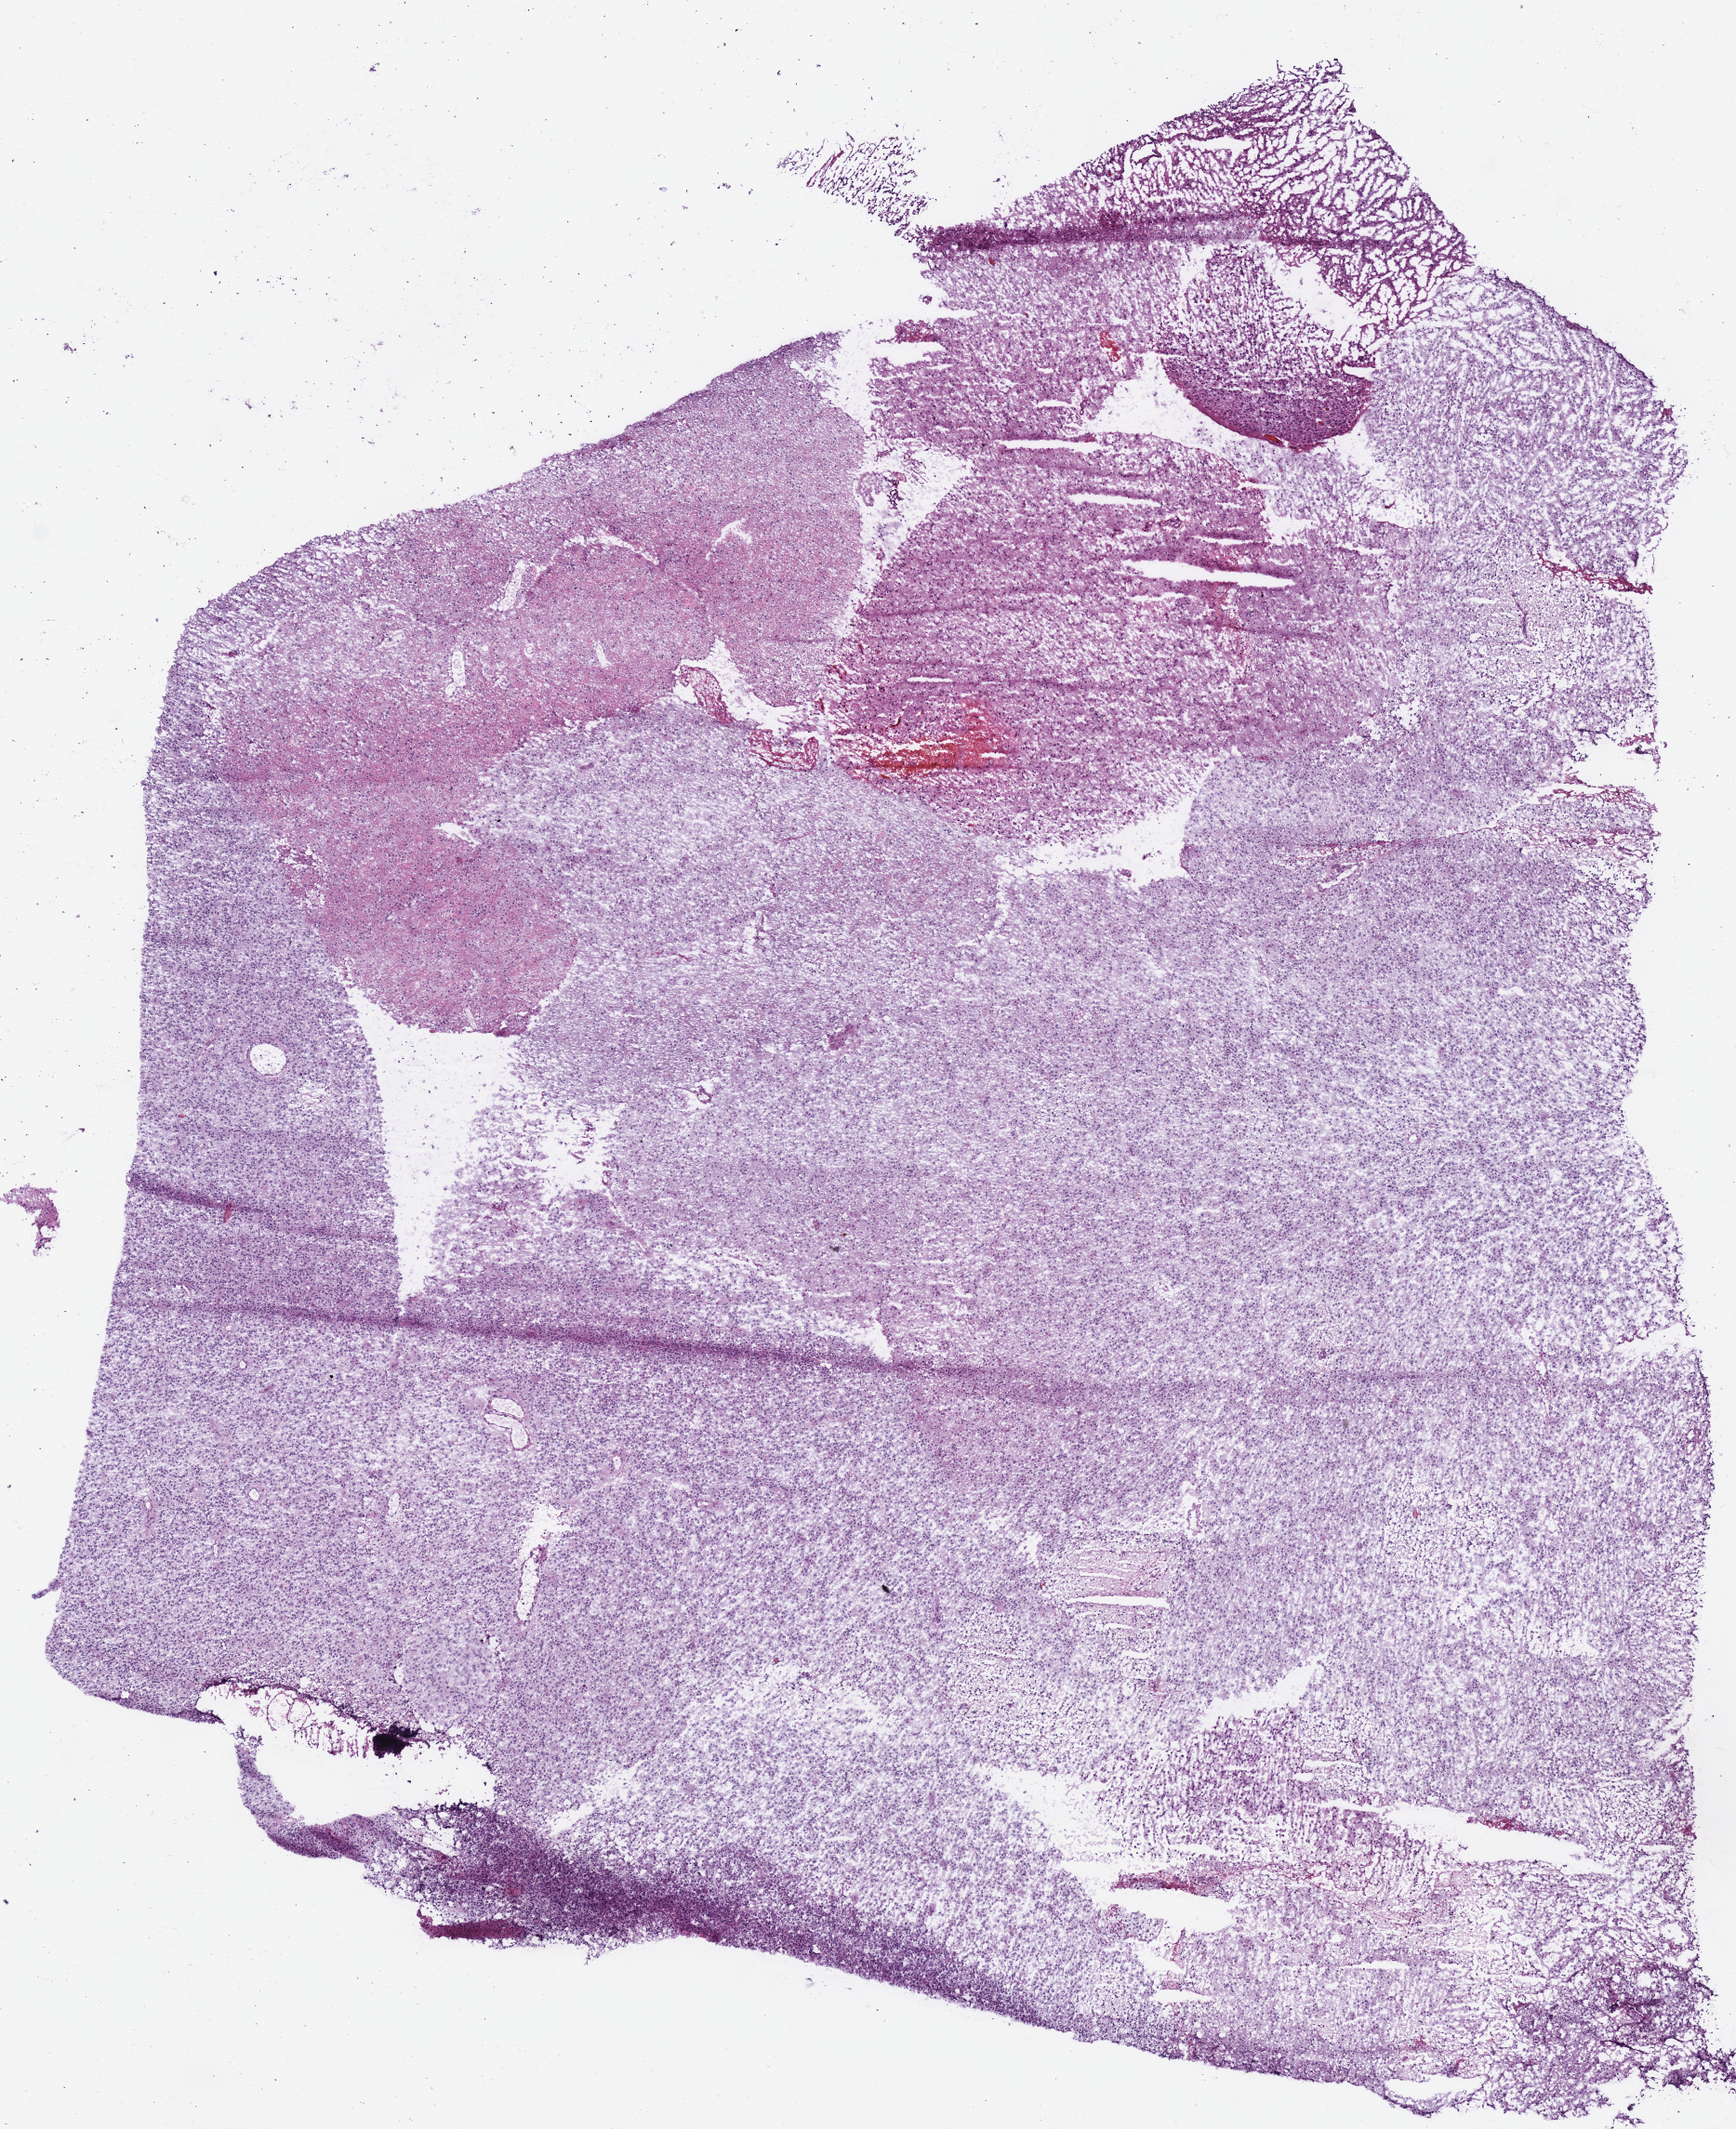
Hematoxylin and eosin (H&E) stained whole-slide image, whole scanned area (about 7.3 x 9.0 mm, acquisition: 40x scan) shown as a low-resolution overview. Frozen section. Brain, primary tumour sample. Male, age 39 years at initial diagnosis. Histologic grade: G2 (moderately differentiated). Pathologist review of this section (percent, as recorded): tumour cells 100%, tumour nuclei 85%, normal cells 0%, stromal cells 0%, necrosis 0%.
Diagnosis: Oligodendroglioma, NOS (cerebrum). Laterality: left.